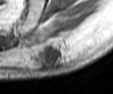
MRI of an extremity soft-tissue mass, one axial slice; position 13 of 42 along the scan axis; MR volume resampled by the dataset authors to the PET/CT grid (not the native acquisition matrix); 113 × 94 image matrix. Male patient. Case-level facts recorded for this patient, not image findings: histological type: leiomyosarcoma; grade: intermediate; site of the primary tumour: left pelvis.
Outlined on this slice (expert contour drawn on MRI and transferred to this co-registered scan by the dataset authors):
- gross tumour volume (mass): box from (x=44, y=46) to (x=66, y=67) px